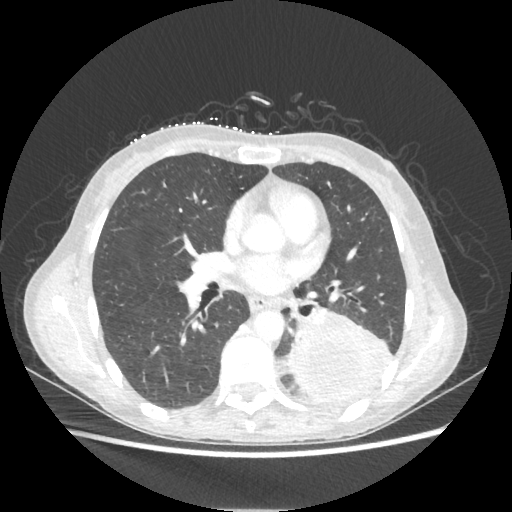
Chest CT, one axial slice; slice 112 of 221 in the series (ordered by position); lung window (W 1500 / L -600 HU); 512 × 512 image matrix. Female patient, age 53 years. Case-level facts recorded for this patient, not image findings: clinical TNM (as recorded): T3 N0 M0.
Outlined on this slice (bounding box drawn by a radiologist):
- lung tumour (recorded histology: adenocarcinoma): box from (x=286, y=311) to (x=394, y=402) px